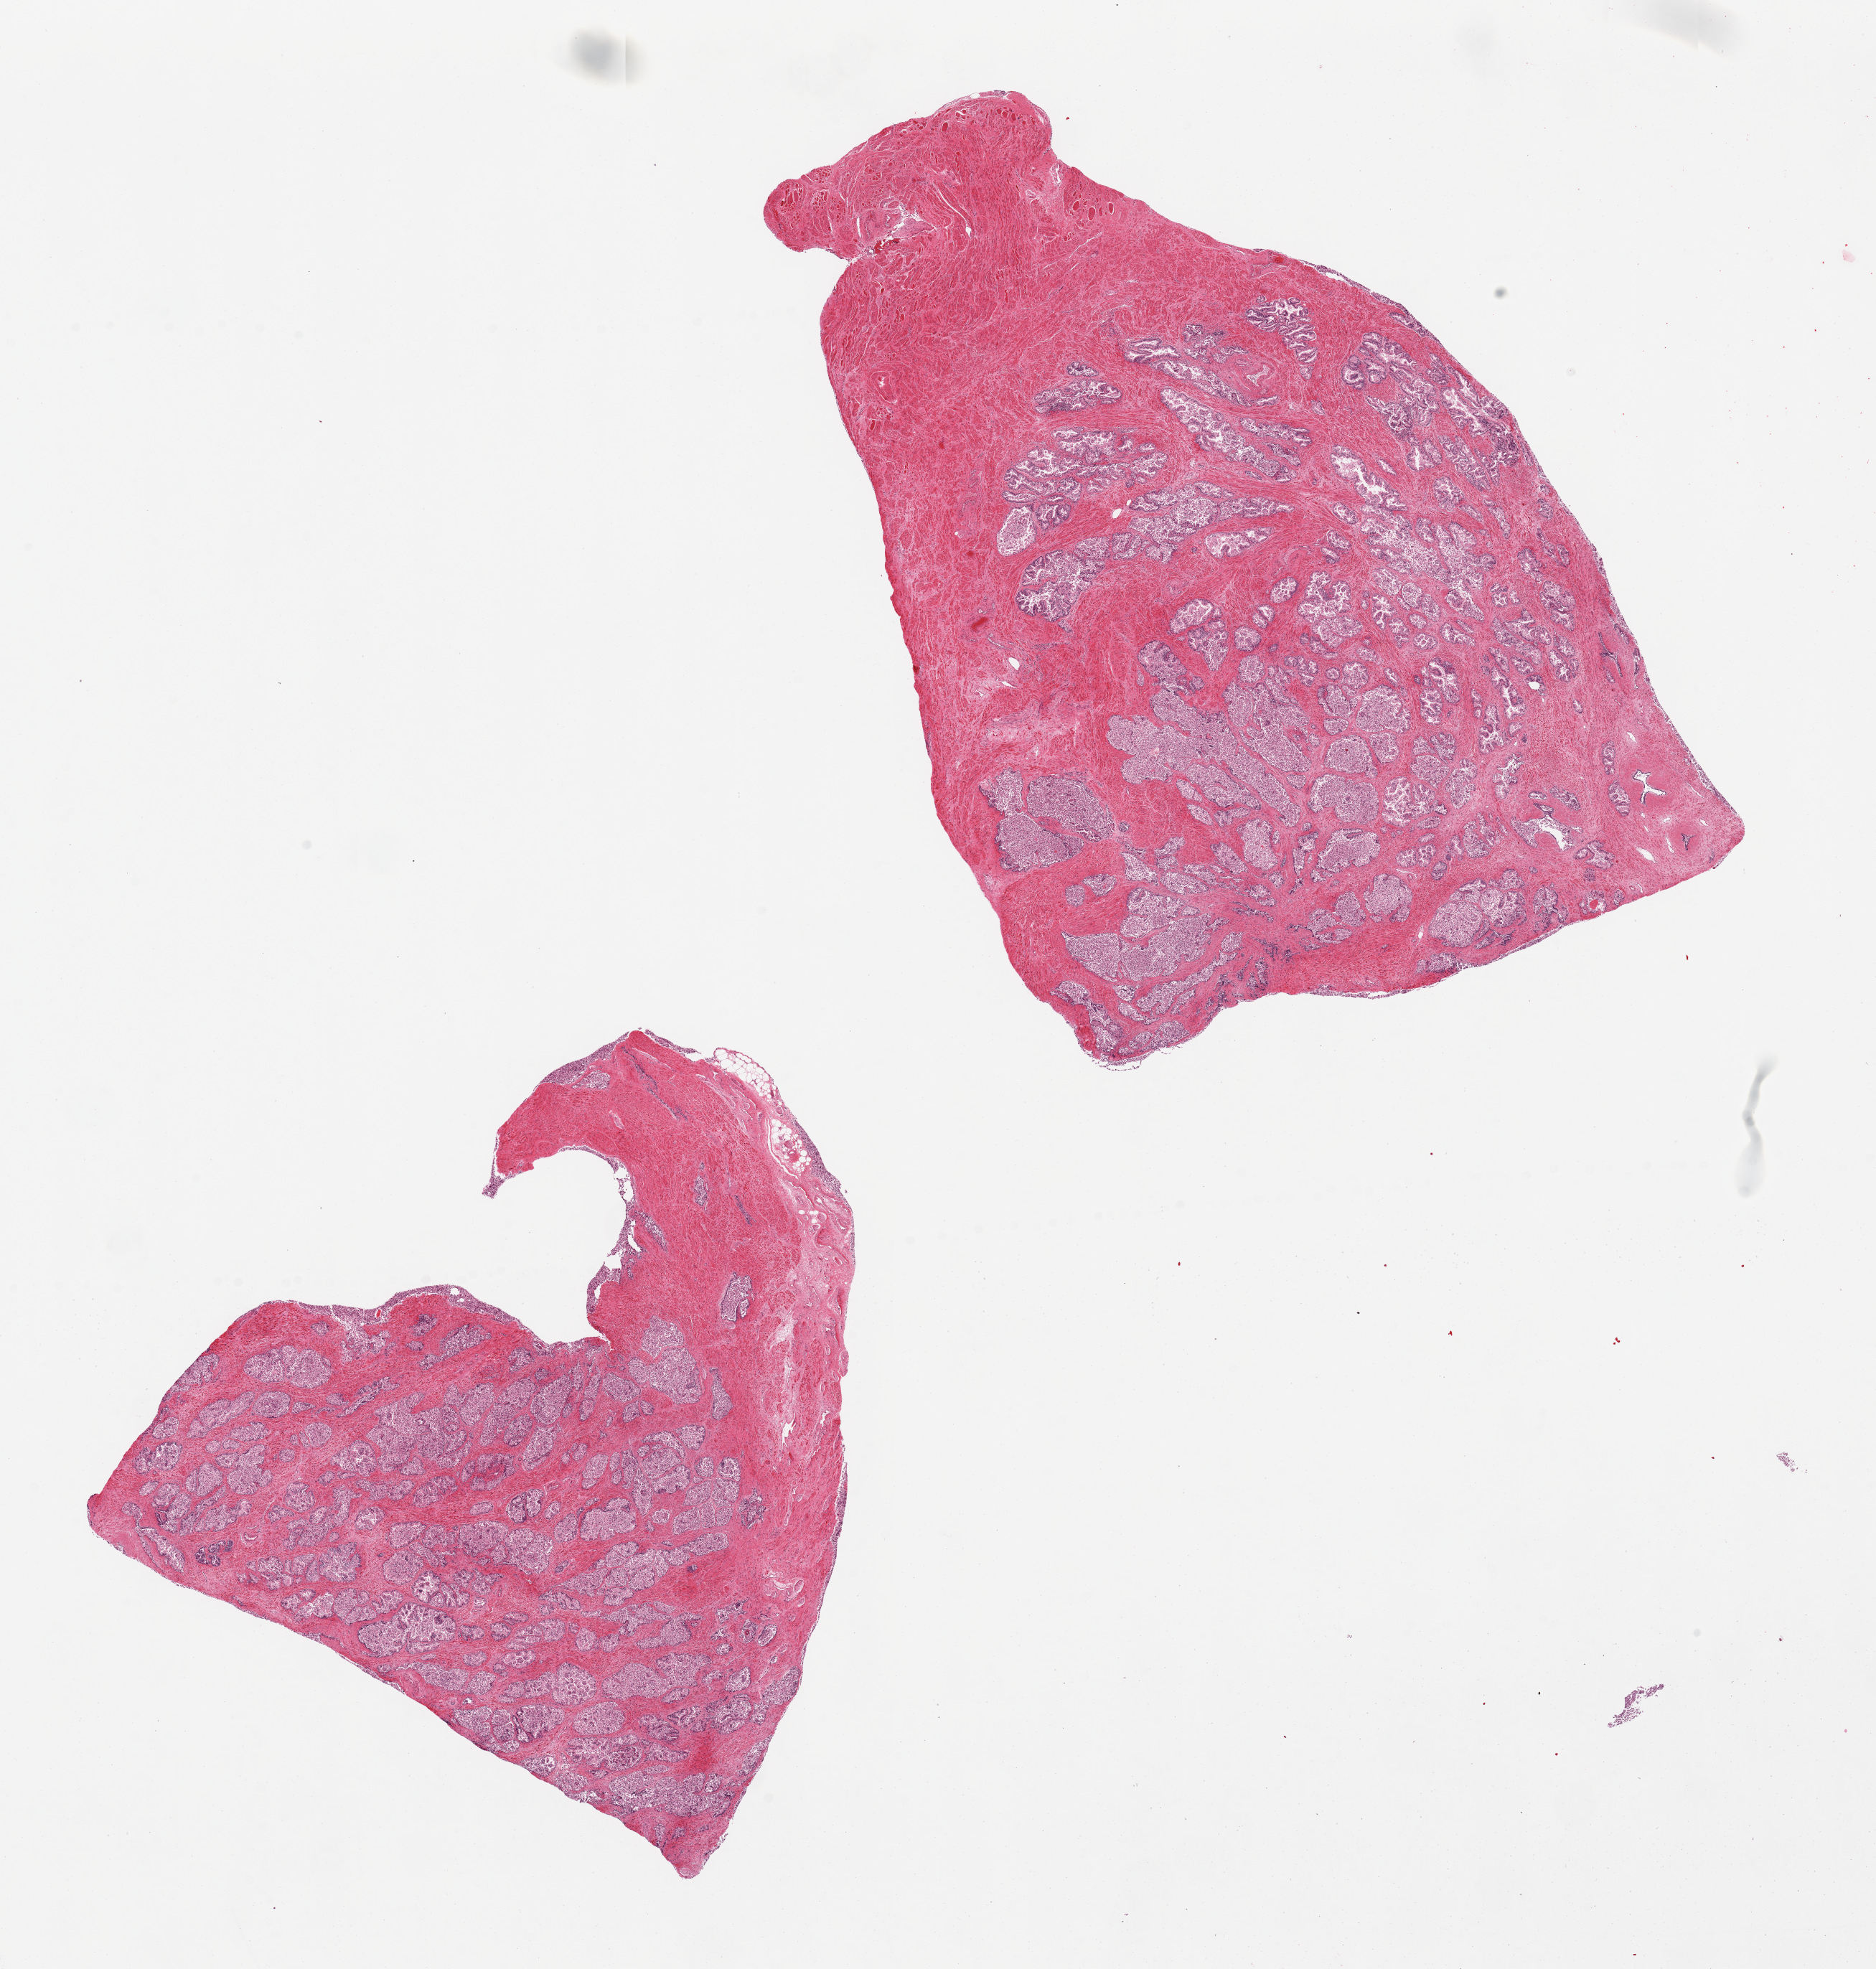
Digitized H&E-stained section — whole scanned area (about 20.7 x 21.7 mm, acquisition: 20x scan) shown as a low-resolution overview. PAXgene-fixed paraffin-embedded (PFPE) section. Sampled site (target tissue): prostate. Tissue donor sample. Donor: male.
• review note (as recorded): 2 pieces. glands completely autolyzed; stroma preserved